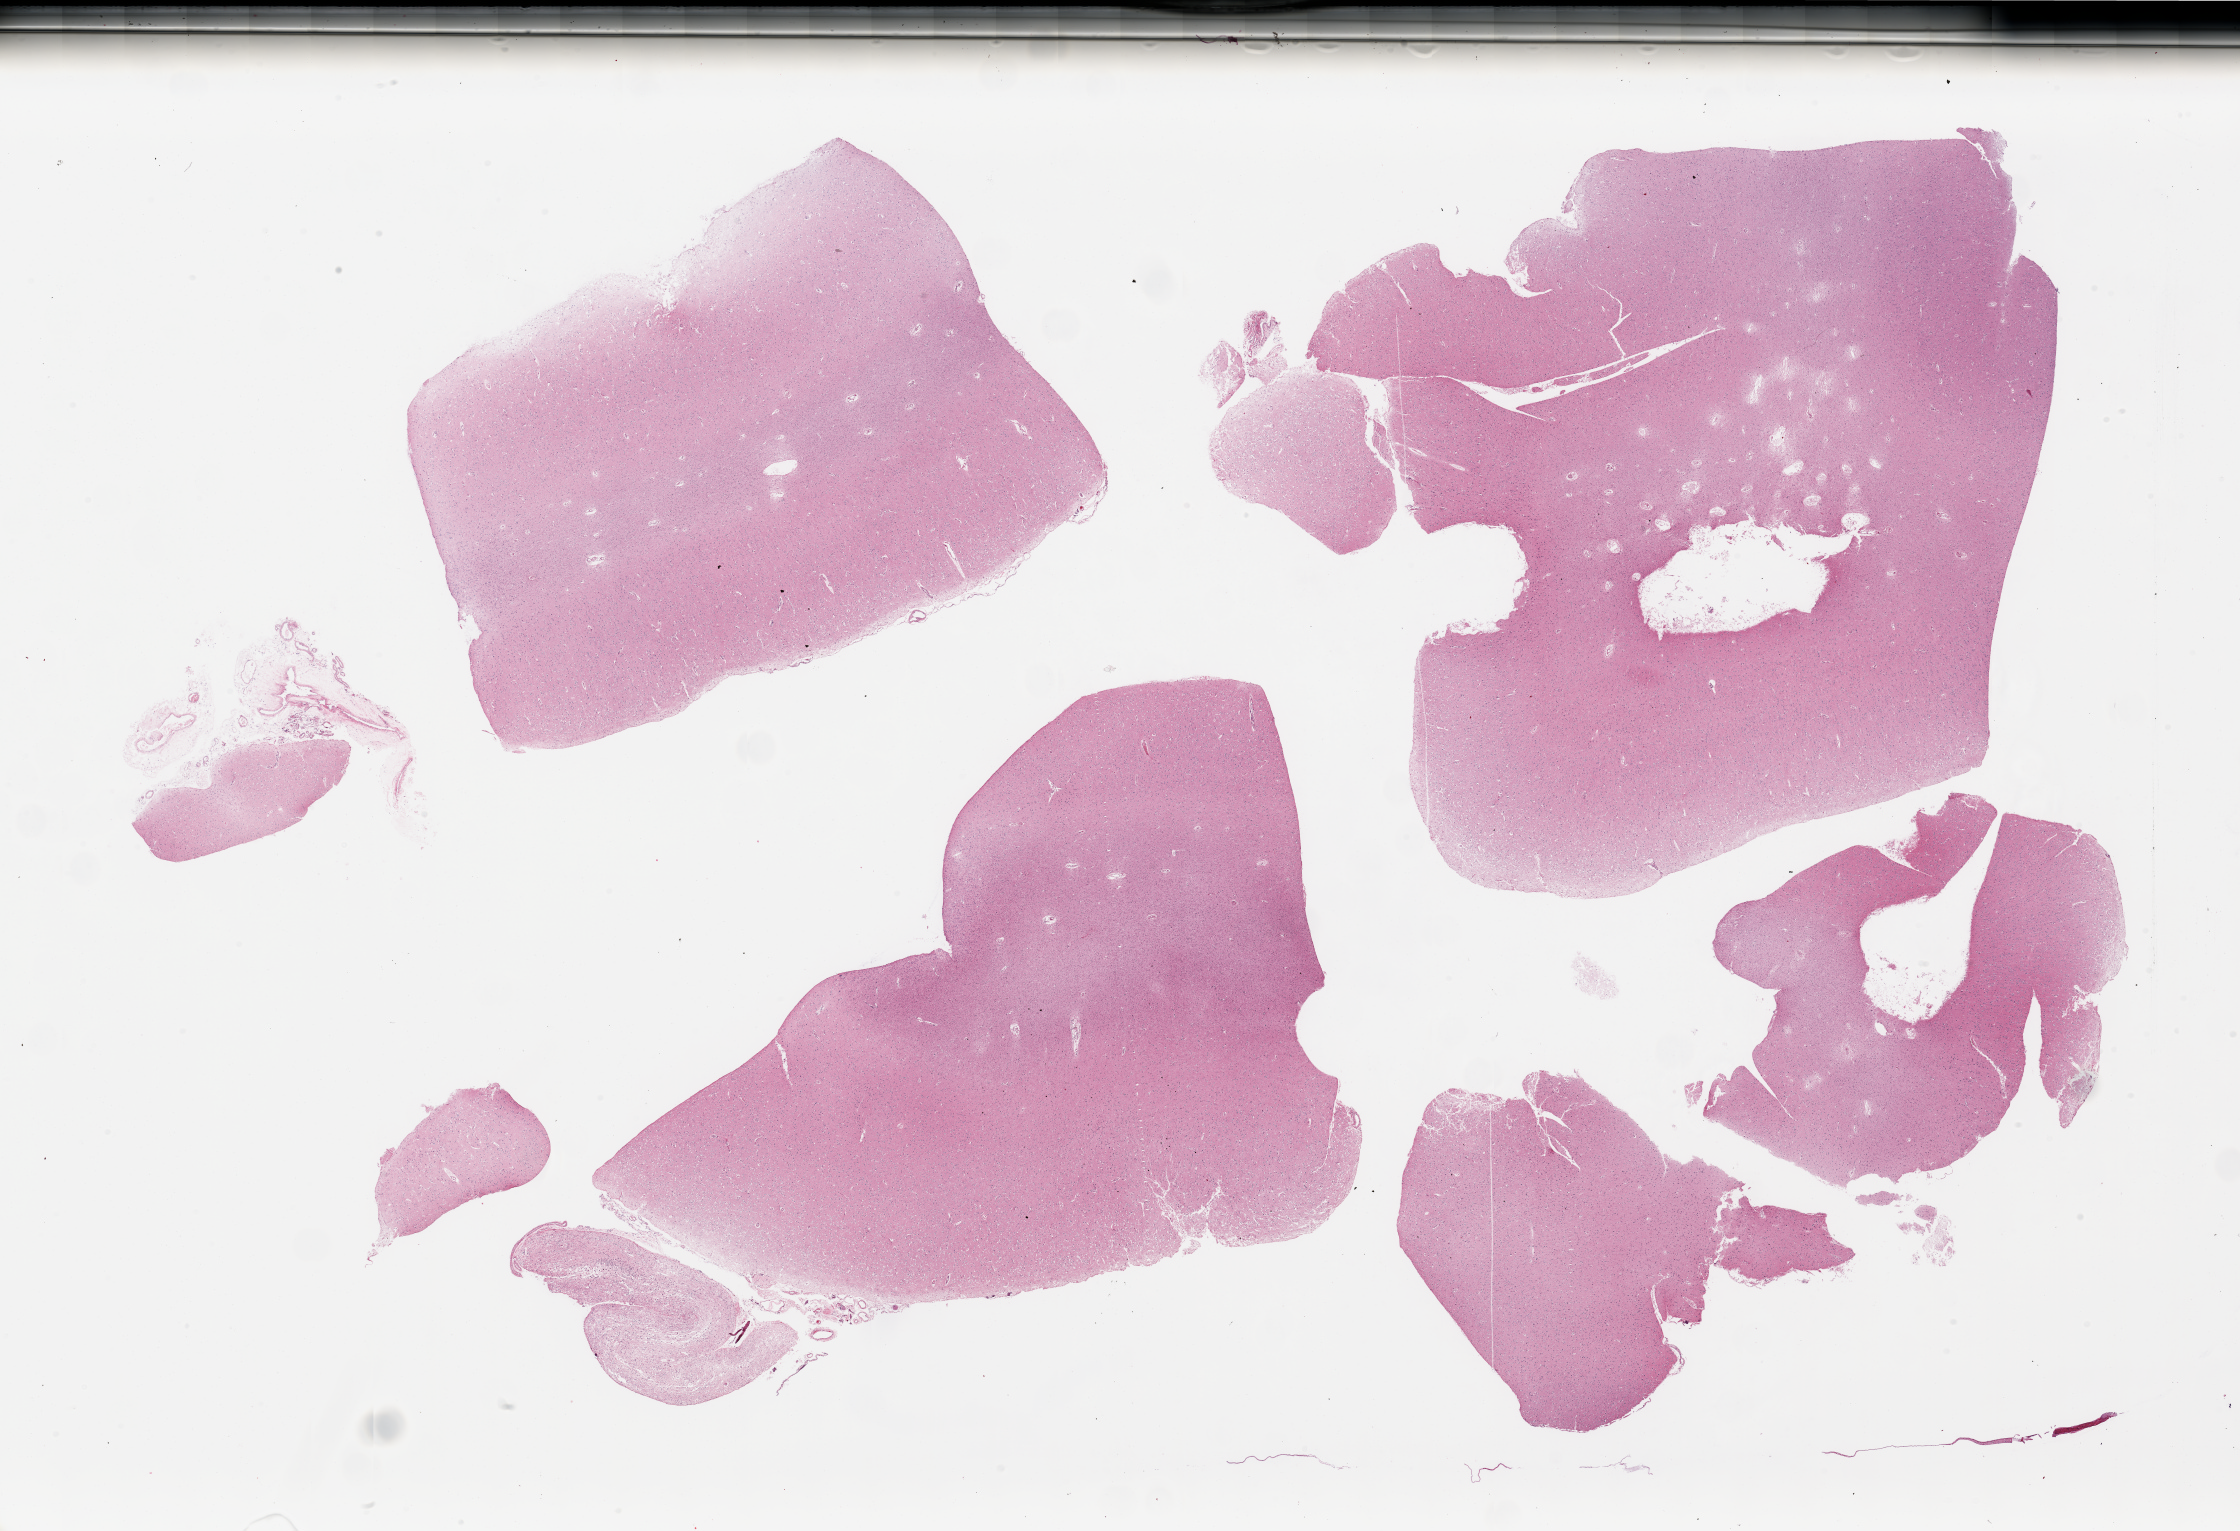
Whole-slide image, haematoxylin and eosin stain, shown as a low-resolution overview of the whole scanned area (about 35.4 x 24.2 mm); PAXgene-fixed paraffin-embedded (PFPE) section; target tissue: cerebral cortex; tissue donor sample. Male donor.
Reviewer comment on this tissue sample: 4 pieces (fragmented); focus of many corpora amylacea.